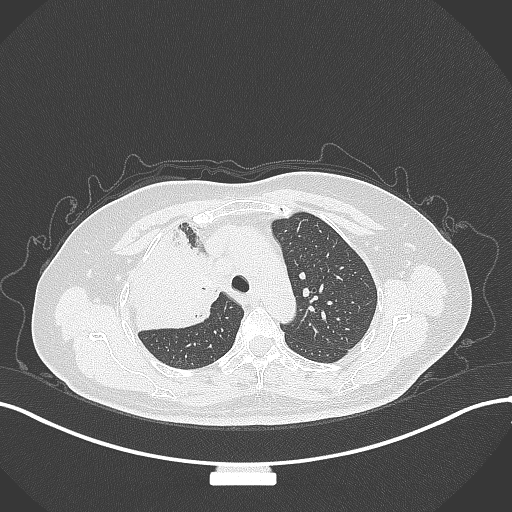
Chest CT, one axial slice. Reconstruction kernel B70f. 120 kVp. Lung window (W 1500 / L -600 HU). 1 mm slice thickness. 512 × 512 image matrix, field of view 400 × 400 mm. Female patient, age 60 years. From the clinical record (not read from this slice): clinical TNM (as recorded): T3 N1 M1.
Structures marked on this image (bounding box drawn by a radiologist):
- lung tumour (recorded histology: adenocarcinoma): box from (x=130, y=225) to (x=226, y=338) px